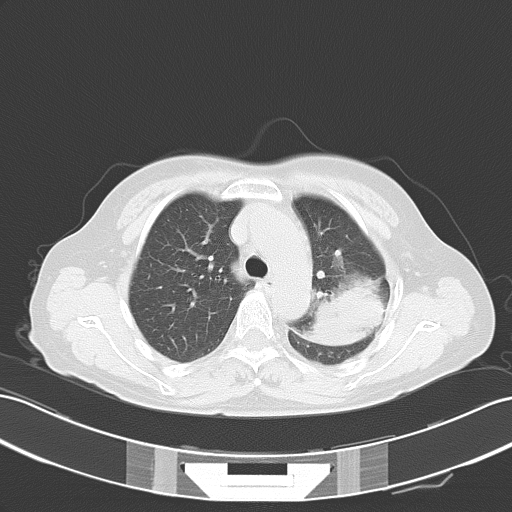
Chest CT, one axial slice; position 36 of 51 along the scan axis; reconstruction kernel B70f; 120 kVp; lung window (W 1500 / L -600 HU); 5 mm slice thickness; 512 × 512 image matrix, field of view 353 × 353 mm. Female patient, age 54 years. From the clinical record (not read from this slice): clinical TNM (as recorded): T3 N1 M0.
Outlined on this slice (rectangle marked by the reading radiologist):
- lung tumour (recorded histology: adenocarcinoma): bounding box (x1, y1, x2, y2) in pixels: (308, 281, 382, 345)